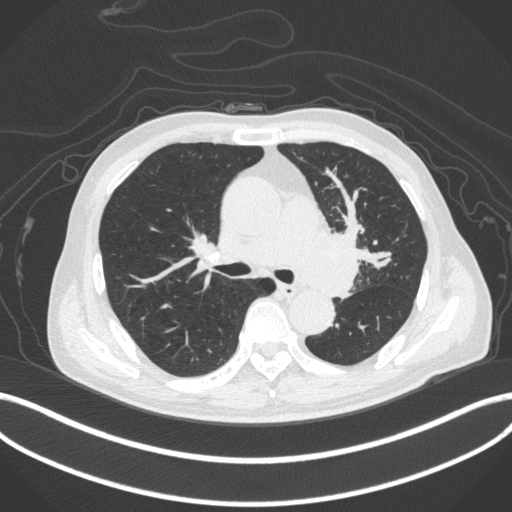
Chest CT, one axial slice; slice 268 of 420 in the series (ordered by position); 120 kVp; lung window (W 1500 / L -600 HU); 1 mm slice thickness; 512 × 512 image matrix, field of view 400 × 400 mm. Male patient, age 77 years. Case-level facts recorded for this patient, not image findings: clinical TNM (as recorded): T3 N1 M0.
Annotated regions visible in this slice (bounding box drawn by a radiologist):
- lung tumour (recorded histology: adenocarcinoma): bounding box (x1, y1, x2, y2) in pixels: (297, 221, 363, 301)